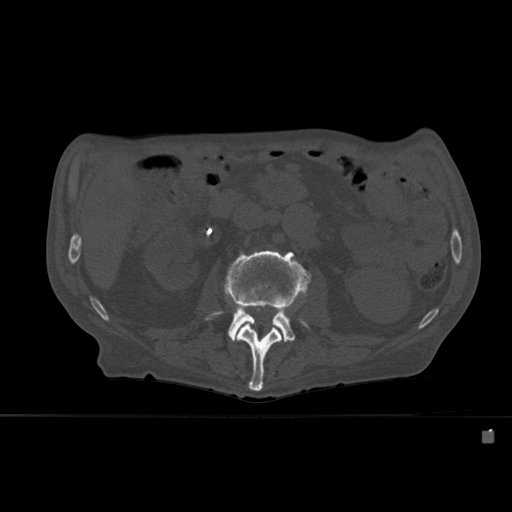
CT including the spine, one axial slice. Slice 223 of 527 in the series (ordered by position). Bone window (W 1800 / L 400 HU). 512 × 512 image matrix, field of view 373 × 373 mm. Male patient, age 78 years. Case-level facts recorded for this patient, not image findings: primary cancer: prostate.
Outlined on this slice (semi-automatic segmentation, software-assisted and operator-edited):
- L2 vertebra: box from (x=225, y=291) to (x=282, y=392) px
- L3 vertebra: (x=210, y=250)–(x=312, y=342)